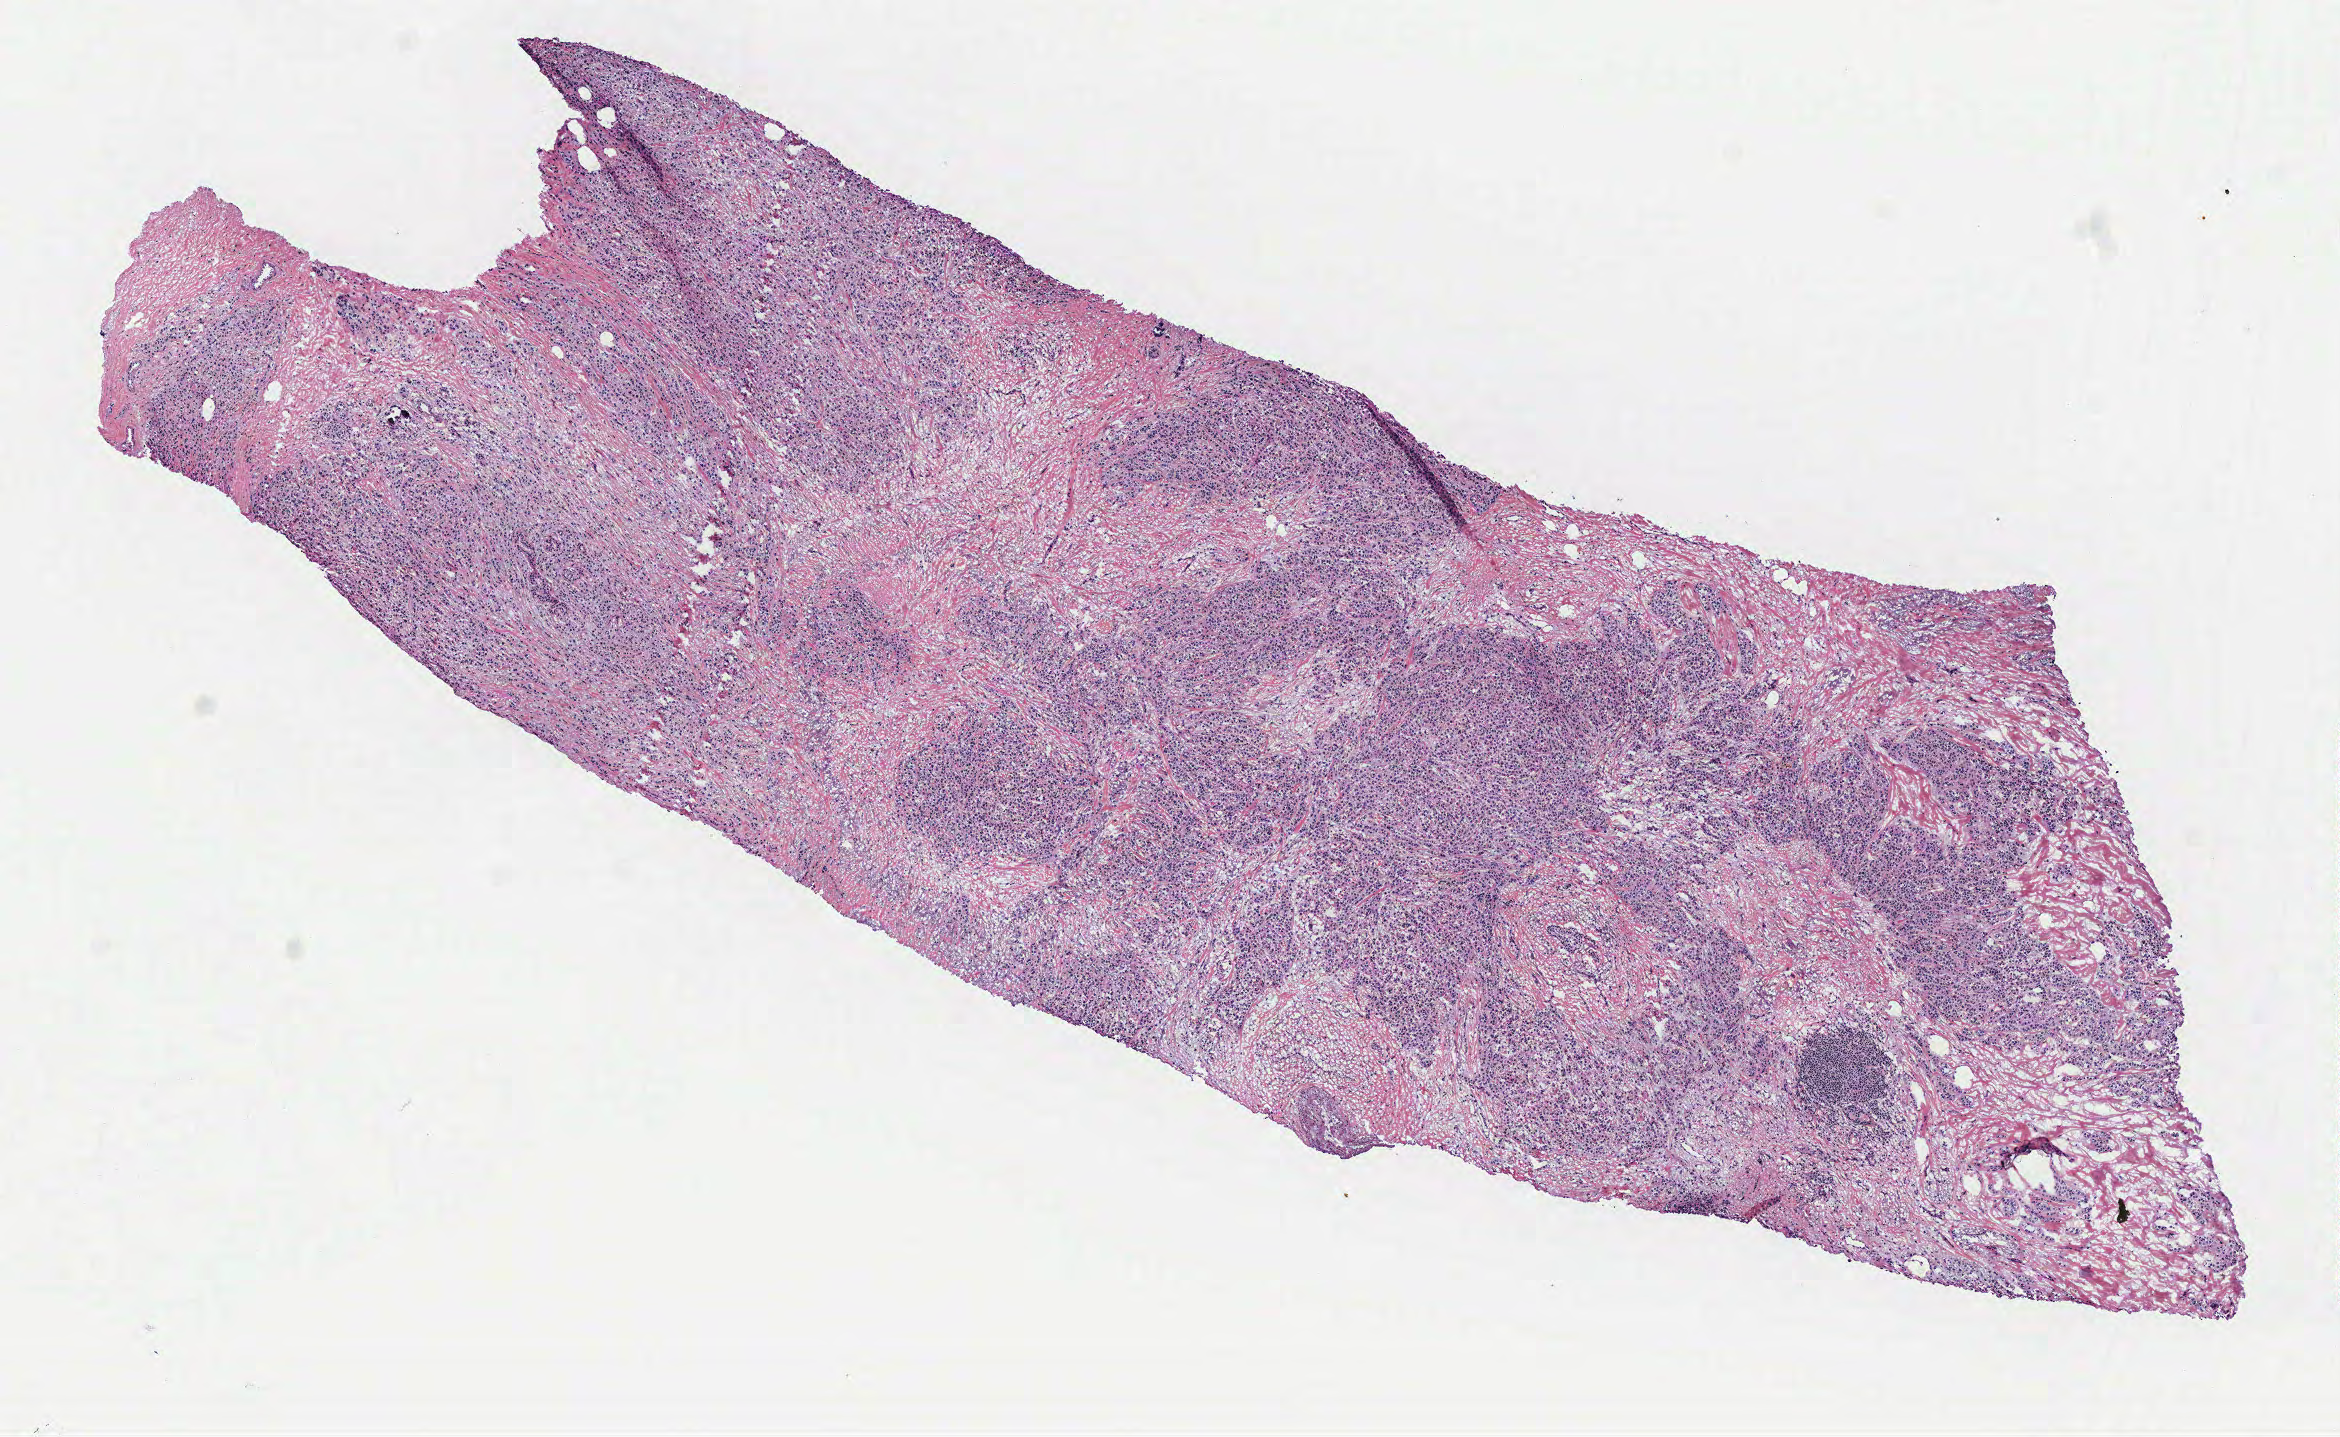
Whole-slide histology image, H&E — shown as a low-resolution overview of the whole scanned area (about 9.4 x 5.8 mm), breast, tissue type not recorded. Female, 78 y/o.
Patient diagnosis: Infiltrating lobular carcinoma, NOS.